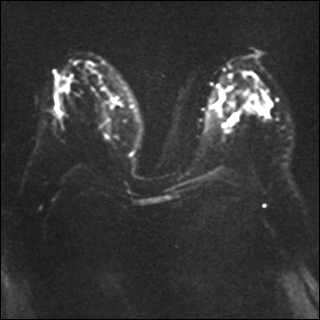
Breast MRI, one axial slice. Position 19 of 41 along the scan axis. Diffusion-weighted series; image 2 of 4 stored at this slice position (different b-values; order by instance number). 1.5 T. 320 × 320 image matrix, field of view 340 × 340 mm. Female patient.
Structures marked on this image (expert manual segmentation):
- tumour on diffusion-weighted imaging: bounding box (x1, y1, x2, y2) in pixels: (256, 104, 263, 113)